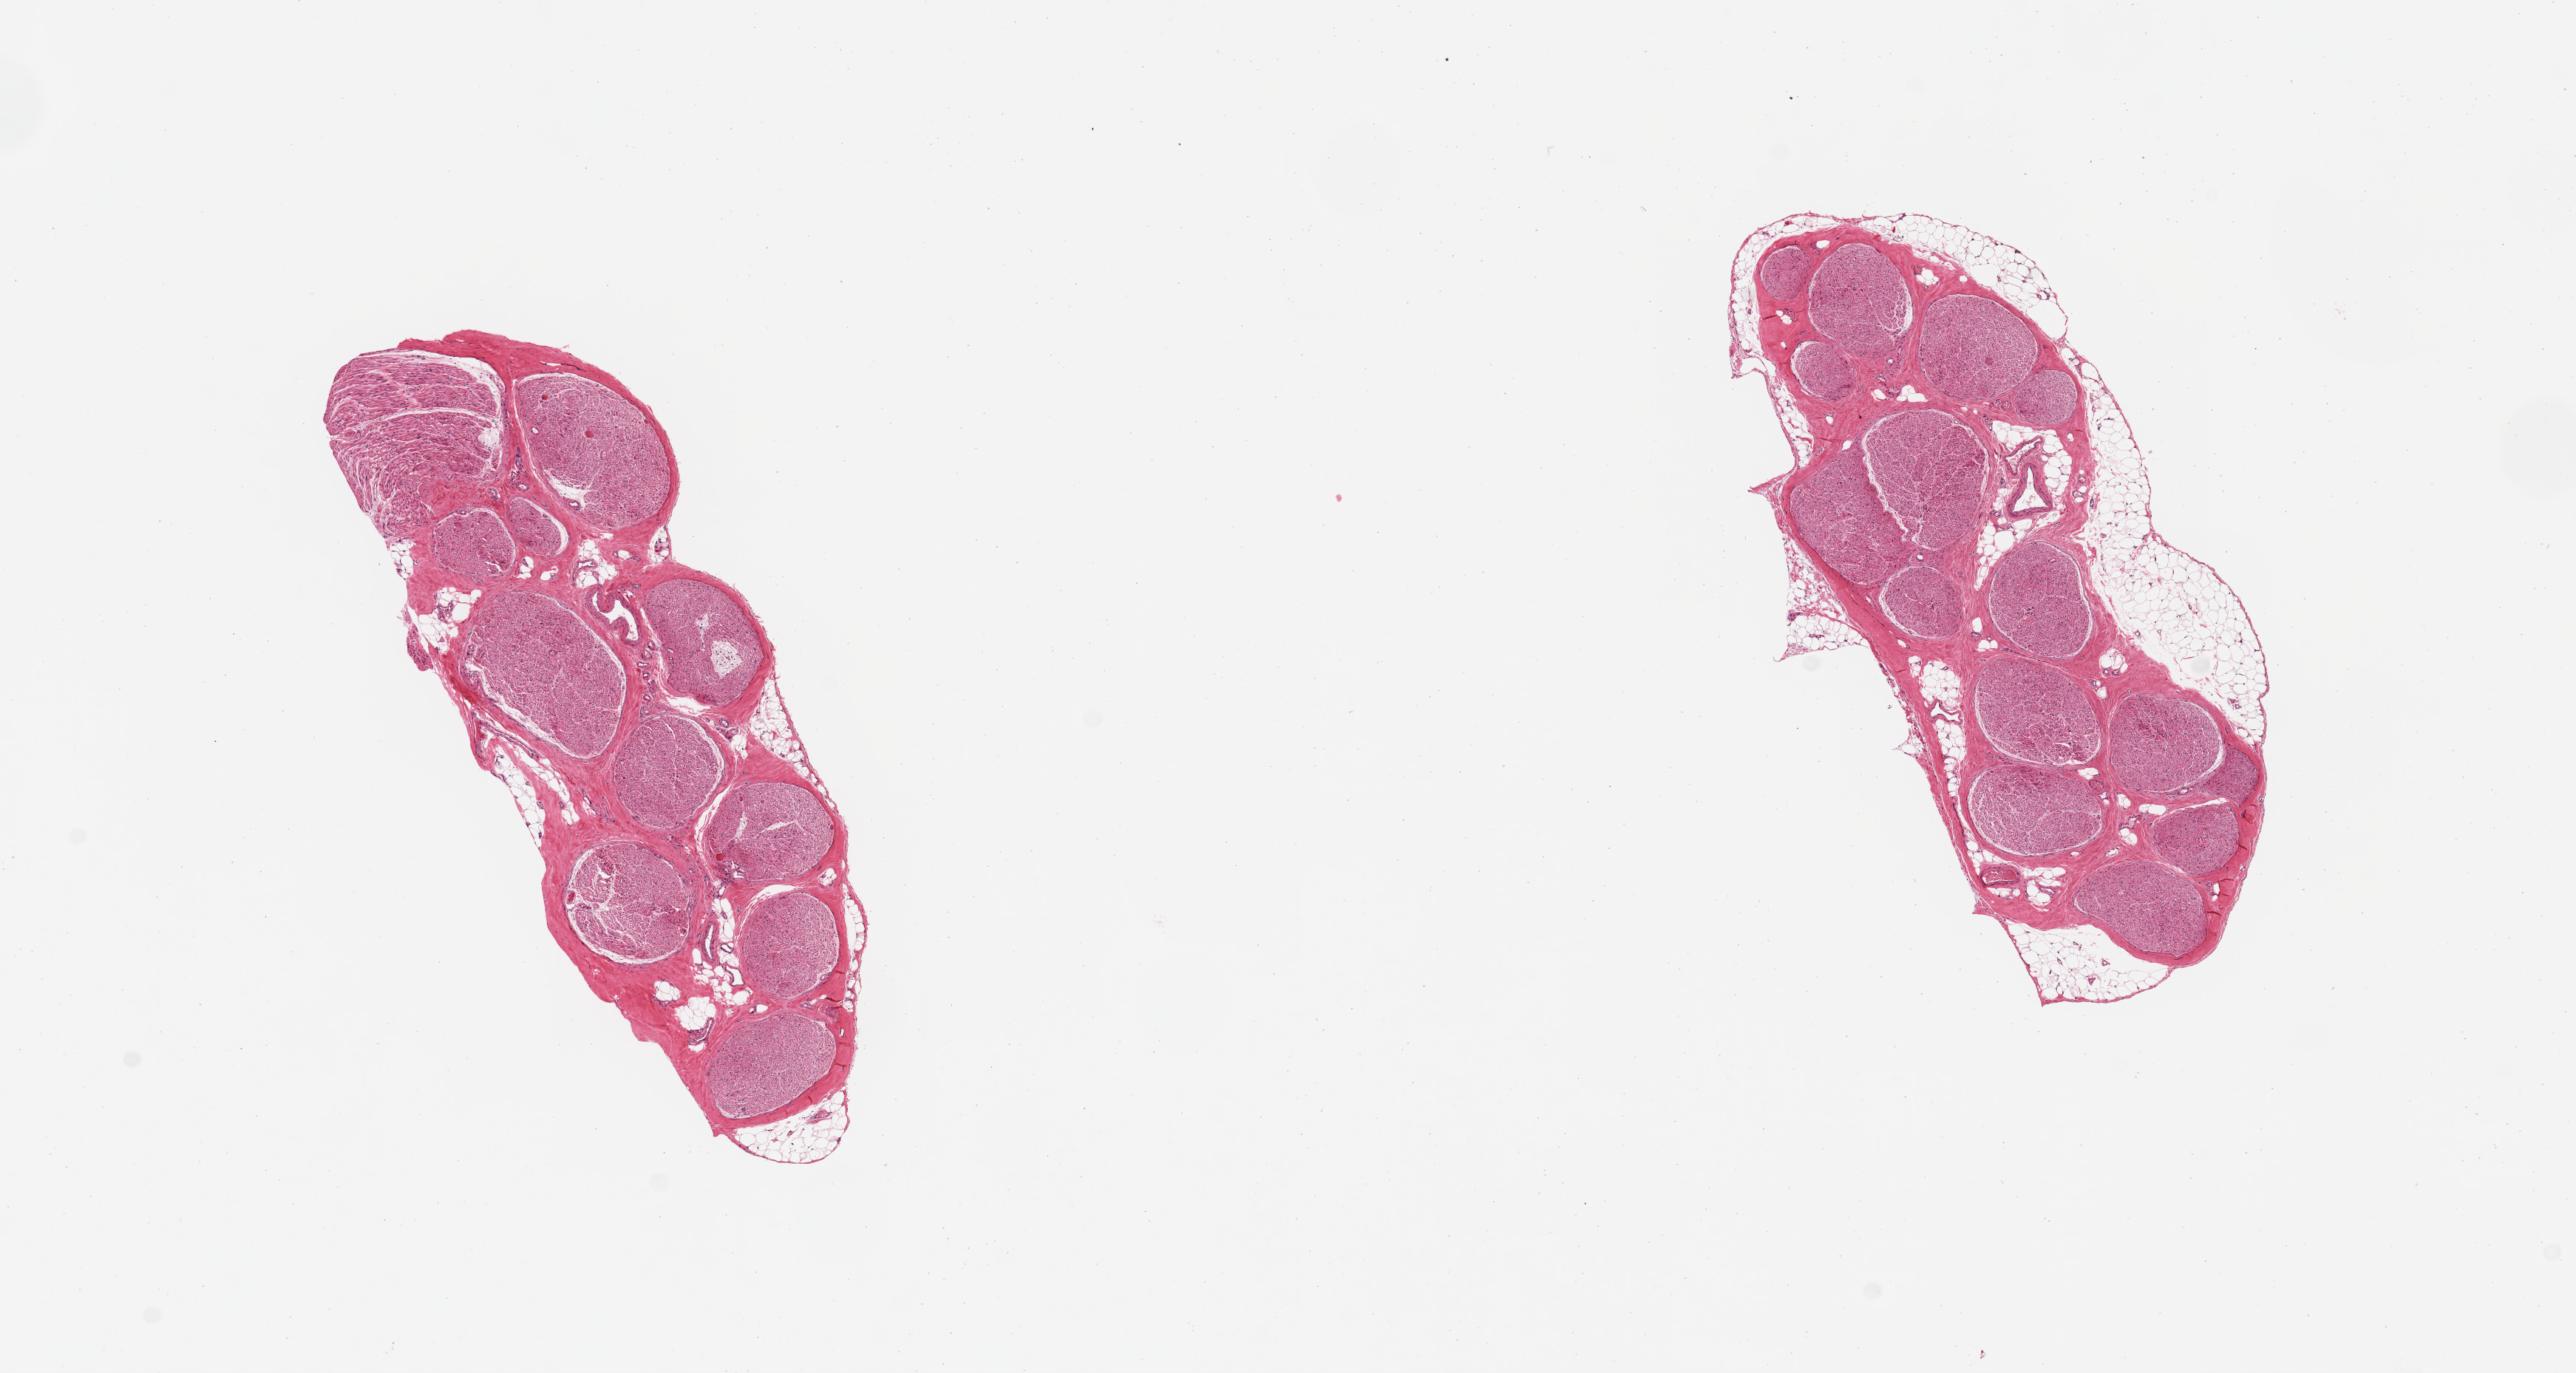
Whole-slide image, hematoxylin and eosin (H&E) stain, brightfield — low-resolution overview of the scanned area, about 13.8 x 7.3 mm, PAXgene-fixed, paraffin-embedded tissue, target tissue: tibial nerve, donor tissue sample. Donor sex: female.
Pathologist's review note for this sample: 2 pieces; includes ~10 and 30% internal/external fat.